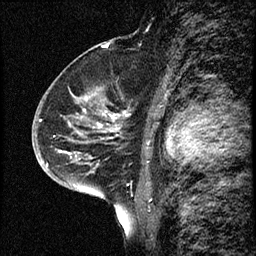
Breast MRI (dynamic contrast-enhanced), one sagittal slice; position 43 of 68 along the scan axis; dynamic contrast-enhanced study with each time point stored as its own series, time point 2 of 3 at this slice position (early post-contrast, ordered by acquisition time); 1.5 T; TE 4.2 ms, TR 17.6 ms; 2 mm slice thickness; 256 × 256 image matrix, field of view 200 × 200 mm. Patient: female, 52 years. From the clinical record (not read from this slice): setting: breast cancer imaged before/during neoadjuvant chemotherapy; receptor status: HER2-positive.
Annotated regions visible in this slice (semi-automatic segmentation, software-assisted and operator-edited):
- analysis volume of interest (the breast-tissue region the enhancement analysis was run in; not a lesion): bounding box [x1, y1, x2, y2] px = [50, 61, 131, 184]
- tumour enhancement mask (voxels above the 100 % enhancement threshold inside the analysis volume of interest): [98, 113, 117, 128]